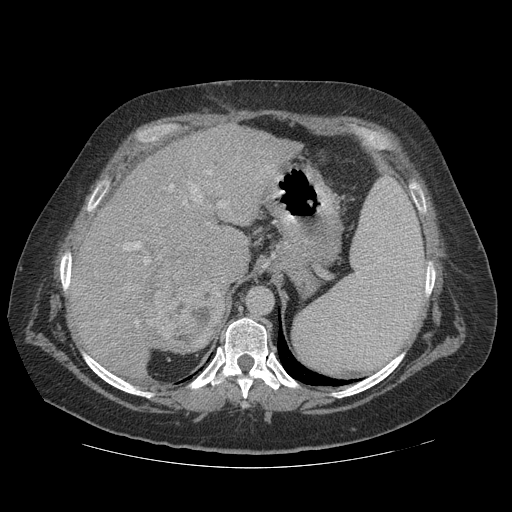
Contrast-enhanced abdominal CT (liver protocol), one axial slice. Slice 84 of 121 in the series (ordered by position). Reconstruction kernel STANDARD. 140 kVp. Soft-tissue window (W 400 / L 40 HU). 512 × 512 image matrix, field of view 420 × 420 mm. From the clinical record (not read from this slice): diagnosis: hepatocellular carcinoma (patient treated with transarterial chemoembolisation; whether this scan precedes or follows treatment is not stated here); TNM stage (as recorded): Stage-IIIA; Child-Pugh class: A; tumour differentiation: well differentiated.
Structures marked on this image (semi-automatic segmentation, software-assisted and operator-edited):
- liver parenchyma outside the tumour (the mass and vessels are separate outlines, so this box may not span the whole liver): bounding box [x1, y1, x2, y2] px = [70, 124, 302, 368]
- mass: [133, 256, 225, 354]
- liver vessels: [84, 166, 271, 339]